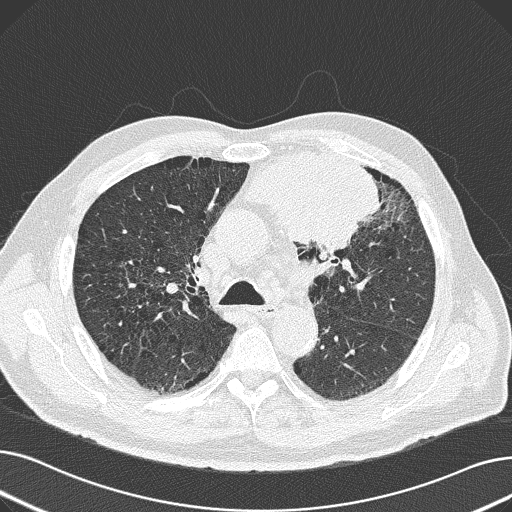
Chest CT (low-dose screening protocol), one axial image, baseline annual screen, lung window (W 1500 / L -600 HU), 120 kVp, slice 65 of 165 in the series. Male participant, aged 69 years at enrolment. Former smoker at enrolment.
• Expert reader's lesion annotation, box from (x=231, y=140) to (x=382, y=251) px.
• Screening reader's record for this exam (one nodule recorded; not confirmed to be the boxed lesion): non-calcified nodule or mass ≥4 mm, left upper lobe, 6 × 10 mm, spiculated (stellate) margins, soft tissue attenuation.
• Later outcome: lung cancer diagnosed 20 days after this screen — non-small cell carcinoma, left upper lobe, poorly differentiated (G3), stage IB (AJCC 6th edition), 100 mm at pathology.